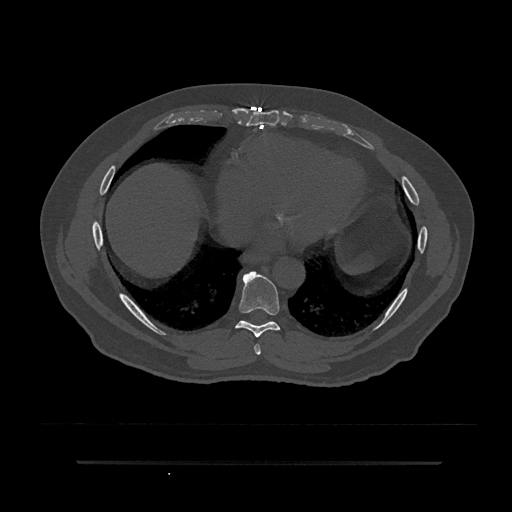
CT including the spine, one axial slice. Slice 423 of 797 in the series (ordered by position). Reconstruction kernel Br40s/3. 120 kVp. Bone window (W 1800 / L 400 HU). 0.5 mm slice thickness. 512 × 512 image matrix, field of view 464 × 464 mm. Patient: male, 59 years. From the clinical record (not read from this slice): primary cancer: bile ducts.
Annotated regions visible in this slice (semi-automatic segmentation, software-assisted and operator-edited):
- T7 vertebra: bounding box (x1, y1, x2, y2) in pixels: (254, 344, 261, 355)
- T8 vertebra: (235, 271, 280, 338)